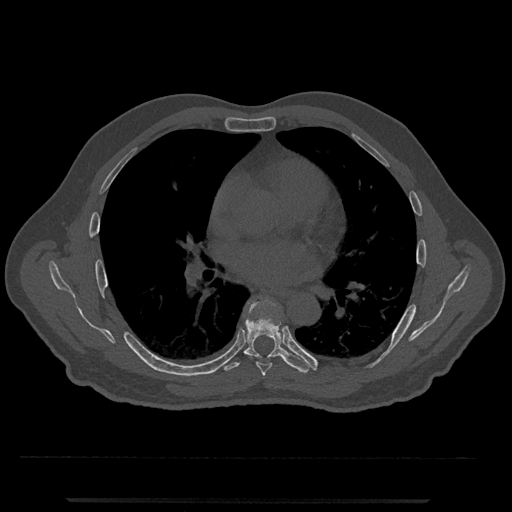
CT including the spine, one axial slice. Position 708 of 797 along the scan axis. Reconstruction kernel Br40s/3. 120 kVp. Bone window (W 1800 / L 400 HU). 0.5 mm slice thickness. 512 × 512 image matrix. Patient: male, 63 years. From the clinical record (not read from this slice): primary cancer: prostate.
Annotated regions visible in this slice (semi-automatic segmentation, software-assisted and operator-edited):
- T6 vertebra: bounding box [x1, y1, x2, y2] px = [256, 362, 272, 376]
- T7 vertebra: [220, 297, 314, 373]